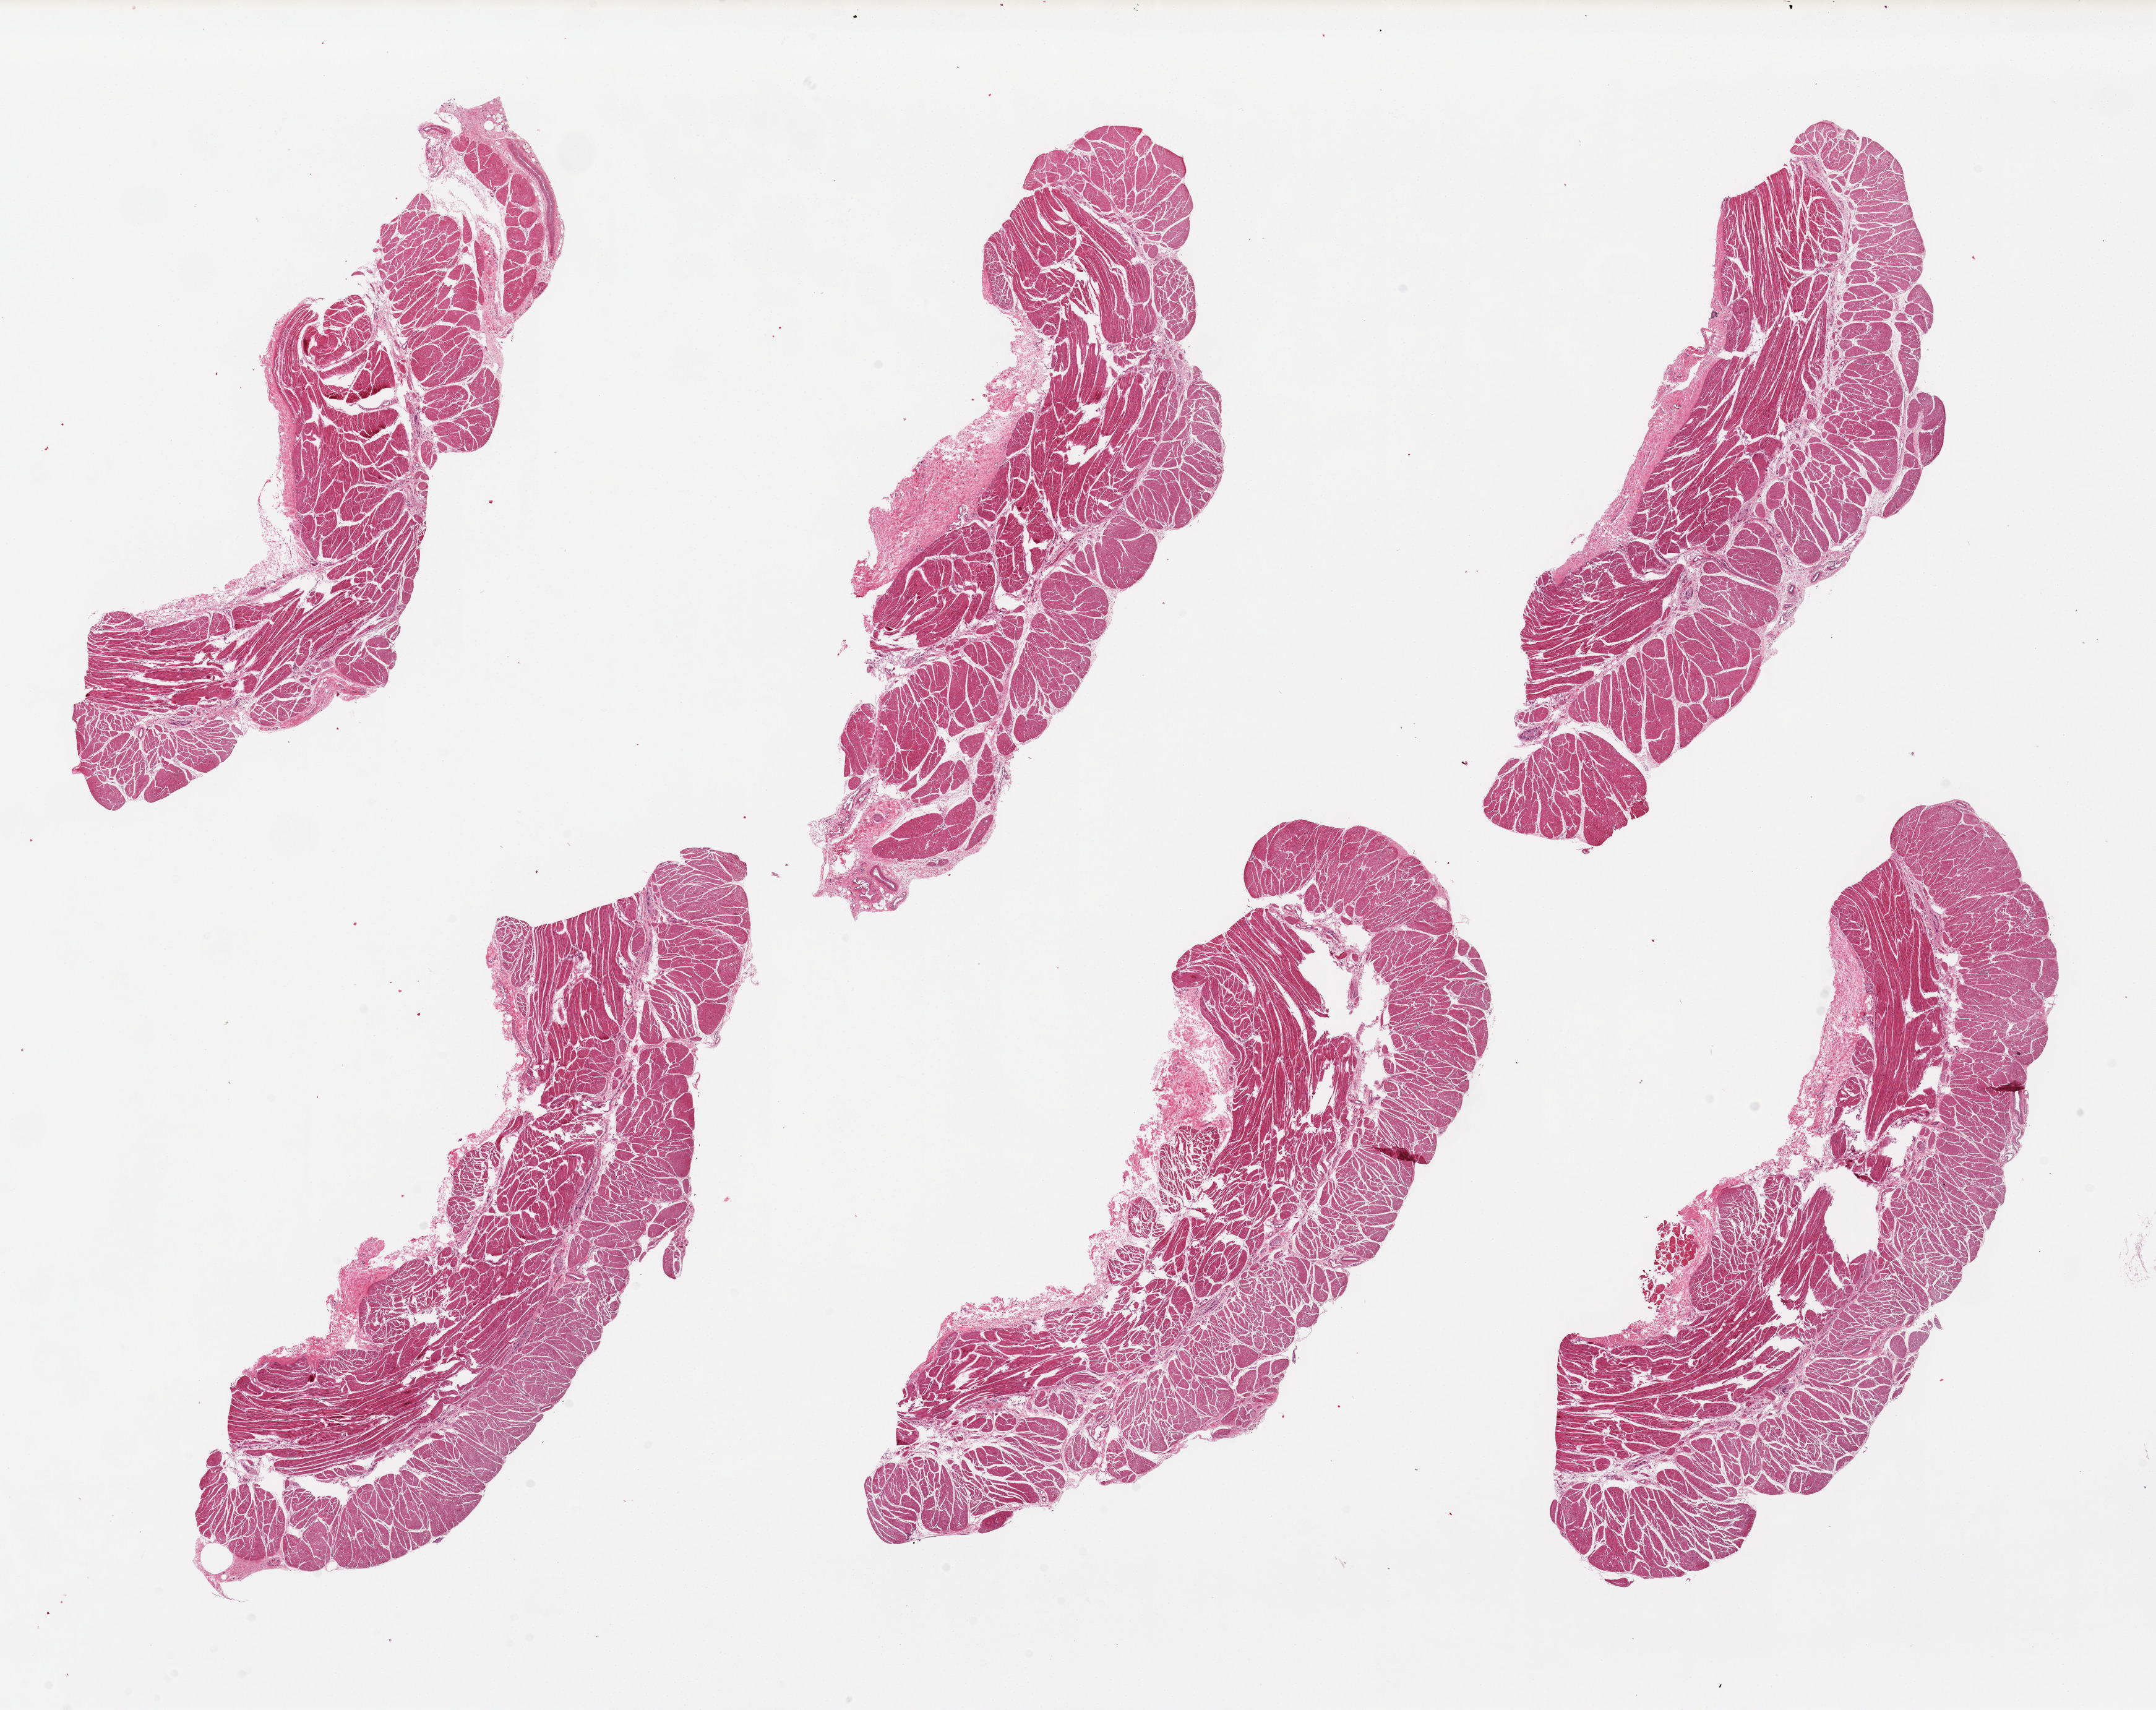
Whole-slide image, H&E stain — shown as a low-resolution overview of the whole scanned area (about 27.6 x 21.9 mm, from a 20x scan), PAXgene-fixed paraffin-embedded (PFPE) section, section of esophageal muscle (target tissue), donor tissue sample.
Pathologist's review note for this sample: 6 pieces; well trimmed.